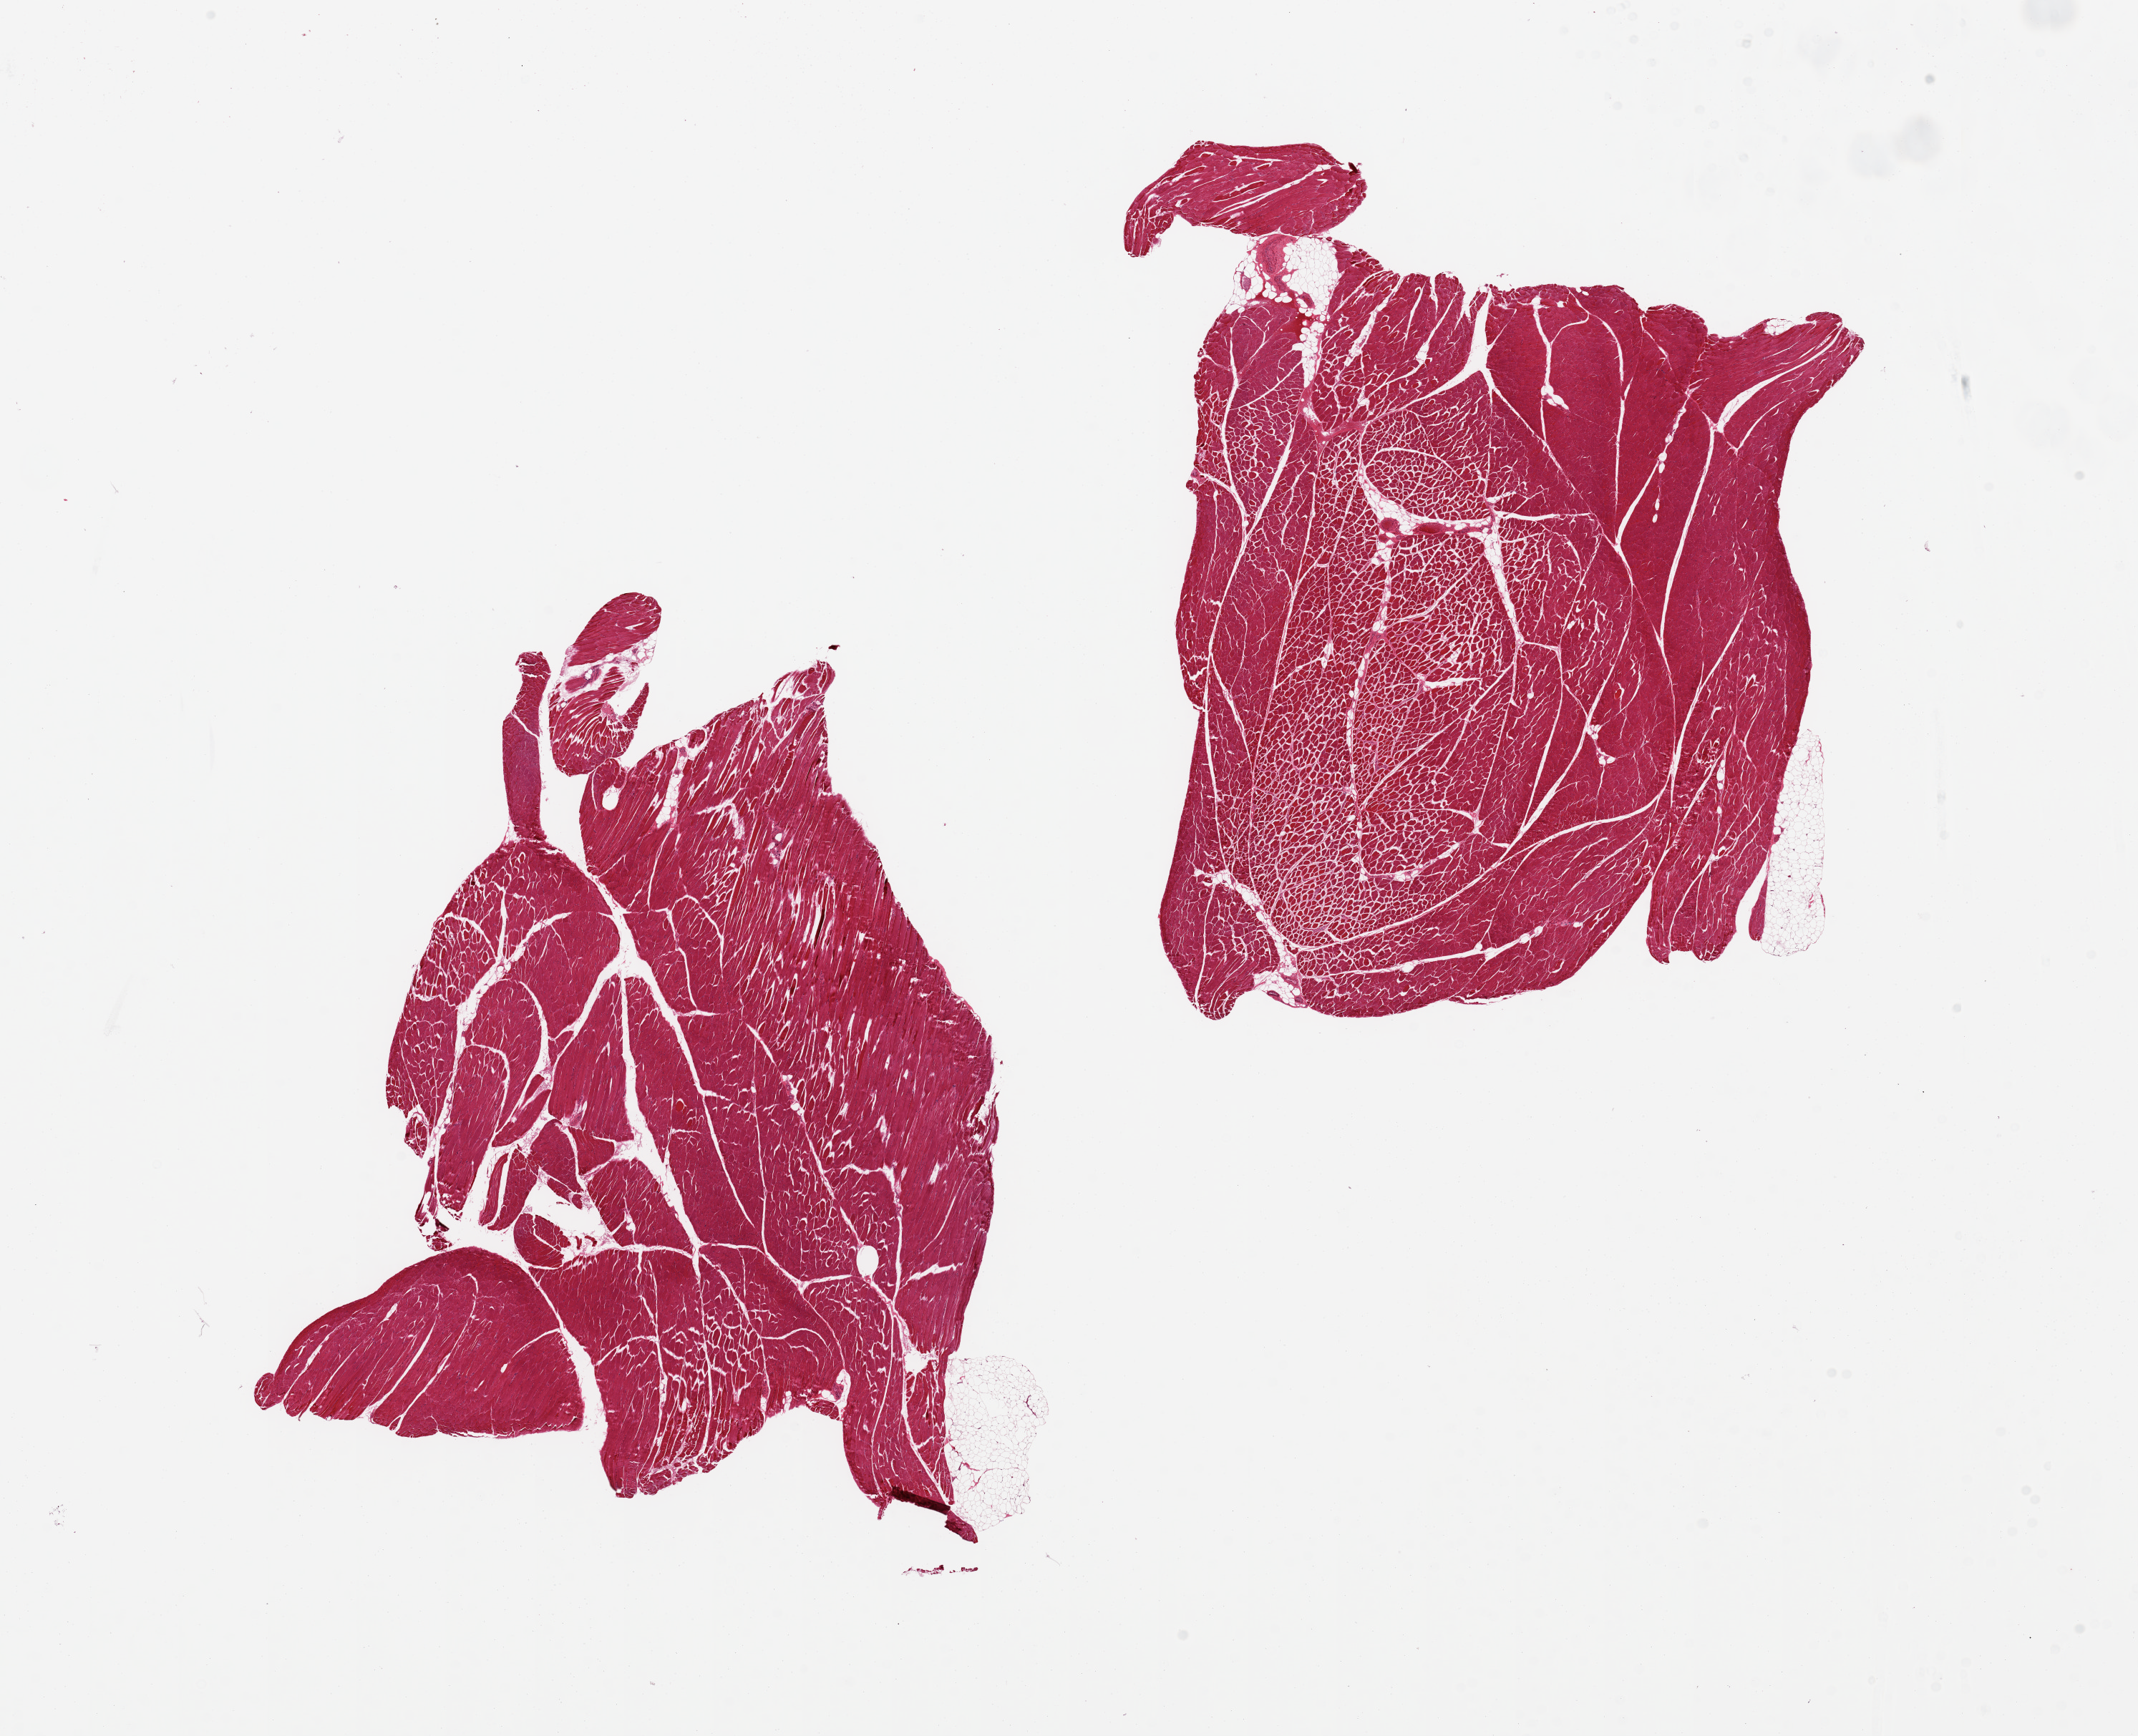
Digitized hematoxylin and eosin (H&E)-stained section — low-resolution overview of the scanned area, about 23.6 x 19.2 mm (acquisition: 20x scan), PAXgene-fixed paraffin-embedded (PFPE) section, target tissue: skeletal muscle, tissue donor sample. Female donor.
Reviewer comment on this tissue sample: 2 pieces, minimal fat.